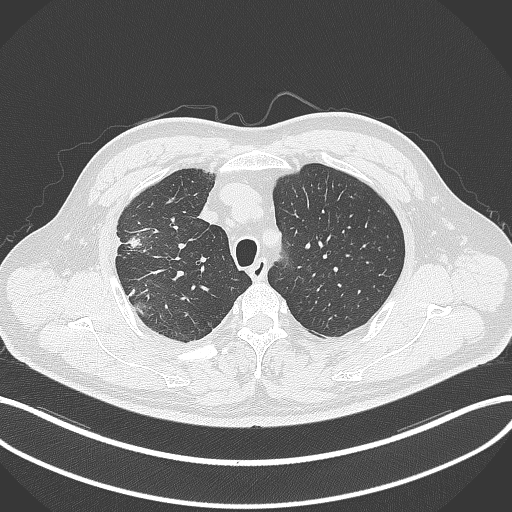
Chest CT, one axial slice. Position 274 of 348 along the scan axis. Reconstruction kernel B70f. Lung window (W 1500 / L -600 HU). 512 × 512 image matrix, field of view 400 × 400 mm. Male patient, age 55 years. Case-level facts recorded for this patient, not image findings: clinical TNM (as recorded): T3 N2 M1.
Annotated regions visible in this slice (rectangle marked by the reading radiologist):
- lung tumour (recorded histology: adenocarcinoma): bounding box (x1, y1, x2, y2) in pixels: (124, 234, 144, 251)